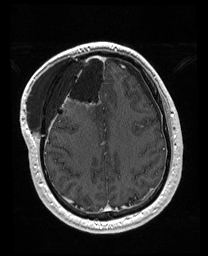
Brain MRI from a brain-tumour surgery series, one axial slice. Slice 62 of 176 in the series (ordered by position). T1-weighted post-contrast. 1 mm slice thickness. 208 × 256 image matrix. Case-level facts recorded for this patient, not image findings: histopathology: Astrocytoma; WHO grade: 4; IDH mutation: yes.
Structures marked on this image (manually delineated by an expert):
- previous resection cavity: bounding box [x1, y1, x2, y2] px = [56, 52, 106, 100]